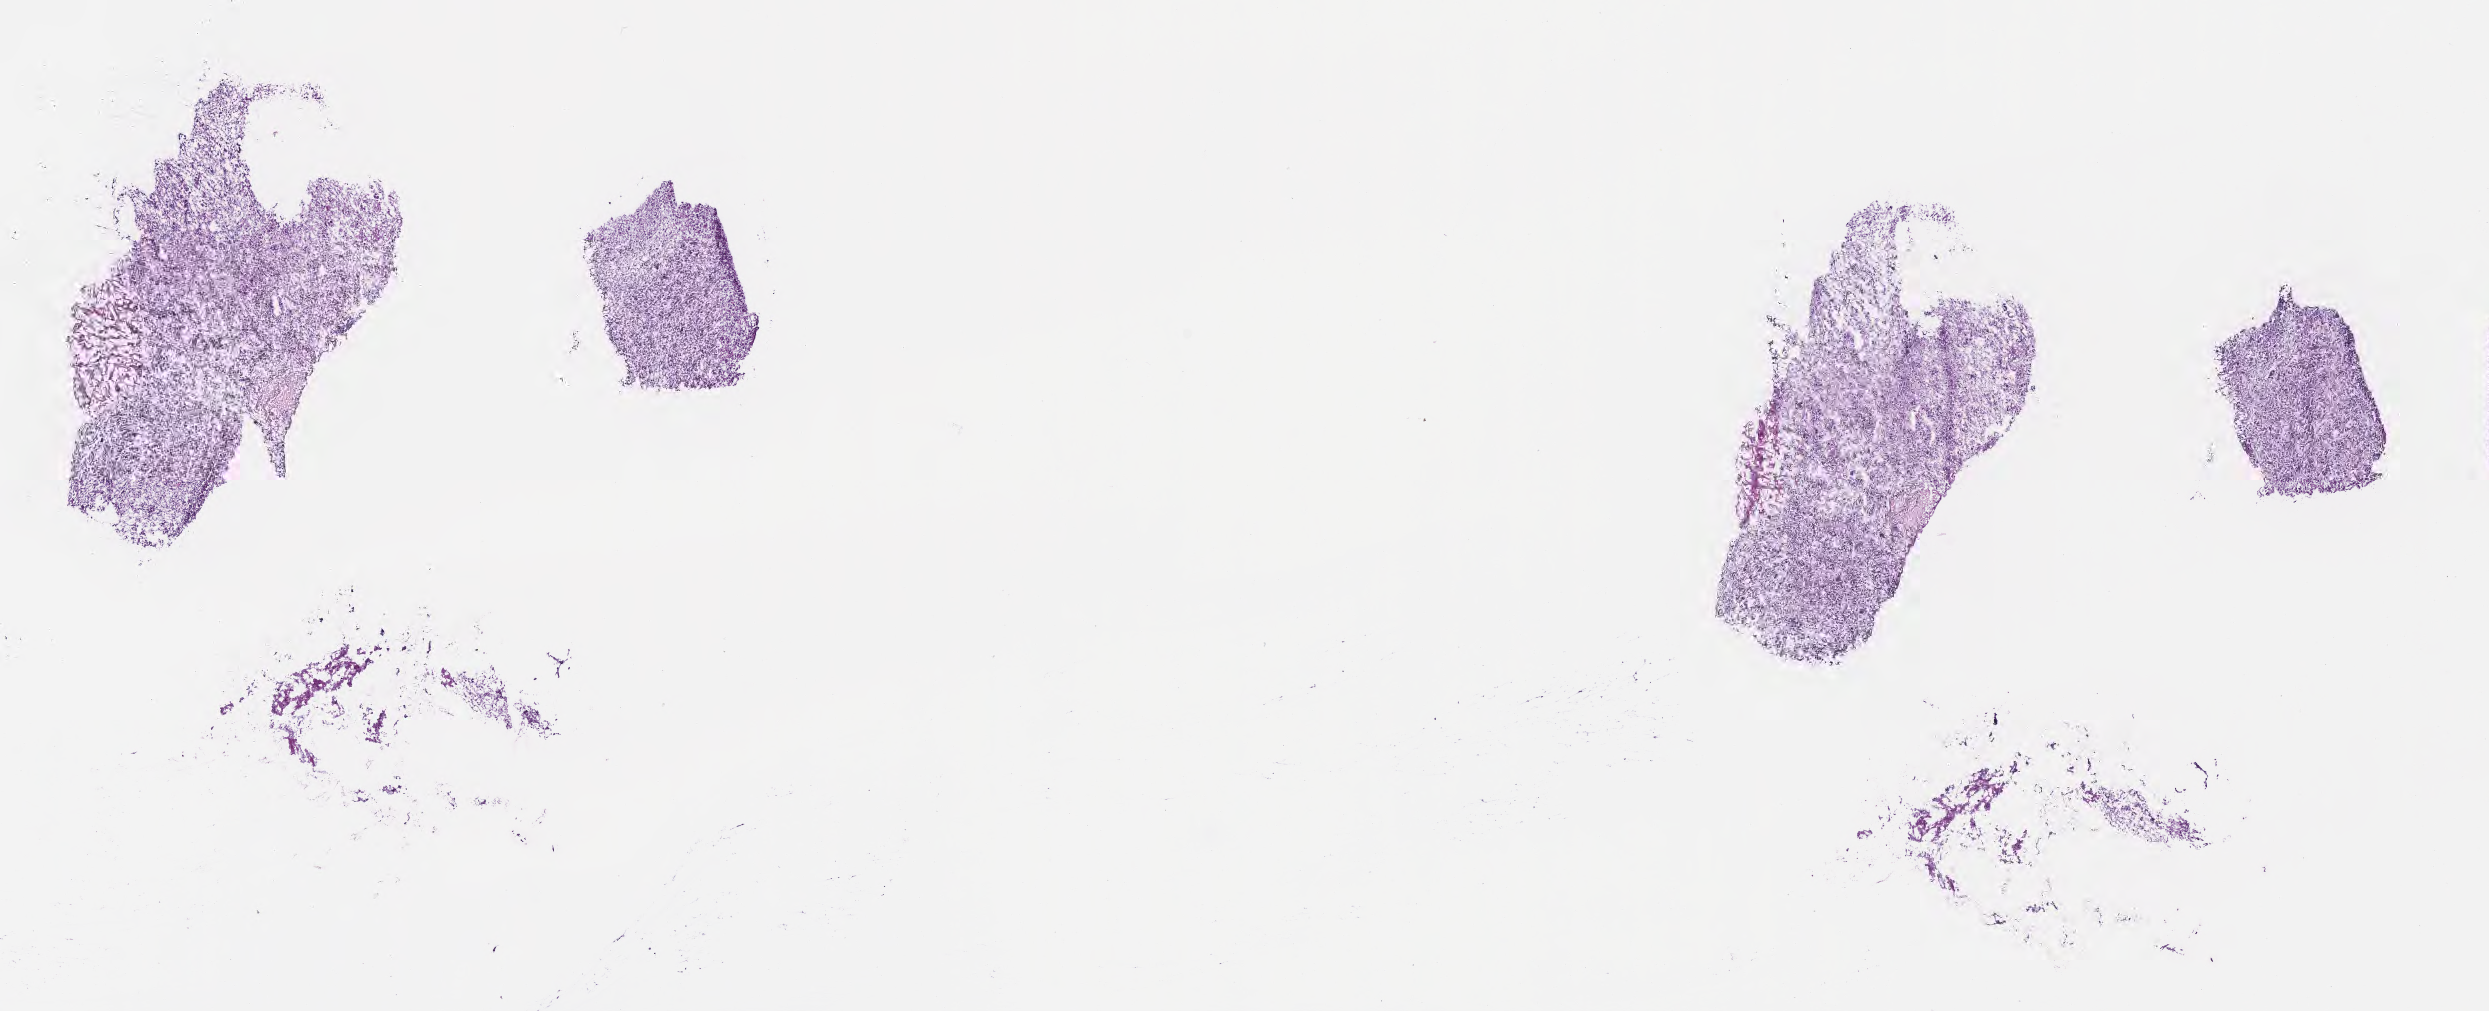
Digitized haematoxylin and eosin-stained section, shown as a low-resolution overview of the whole scanned area (about 20.1 x 8.2 mm), frozen section, specimen: primary tumor, site: brain. Patient: female, age at initial diagnosis 49 years. Slide review estimates, as recorded: tumor cells 85%, tumor nuclei 93%, stromal cells 2%, necrosis 7%, normal cells 6%. Infiltration values recorded for this section: lymphocyte infiltration 0%, monocyte infiltration 0%, neutrophil infiltration 0%.
• section: bottom of the tissue portion
• histologic diagnosis: Glioblastoma, NOS